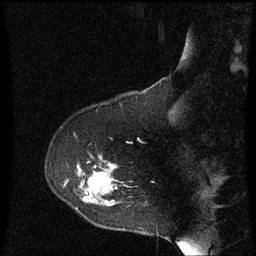
Breast MRI (dynamic contrast-enhanced), one sagittal slice; position 16 of 60 along the scan axis; dynamic contrast-enhanced series, image 2 of 3 at this slice position (ordered by acquisition); 1.5 T; TE 4.2 ms, TR 8.9 ms; 2 mm slice thickness; 256 × 256 image matrix, field of view 200 × 200 mm. Patient: female, 53 years. Case-level facts recorded for this patient, not image findings: setting: breast cancer imaged before/during neoadjuvant chemotherapy; receptor status: HR-positive, HER2-negative.
Annotated regions visible in this slice (semi-automatically segmented with operator editing):
- analysis volume of interest (the breast-tissue region the enhancement analysis was run in; not a lesion): box from (x=76, y=160) to (x=133, y=231) px
- tumour enhancement mask (voxels above the 70 % enhancement threshold inside the analysis volume of interest): (x=84, y=164)–(x=117, y=207)